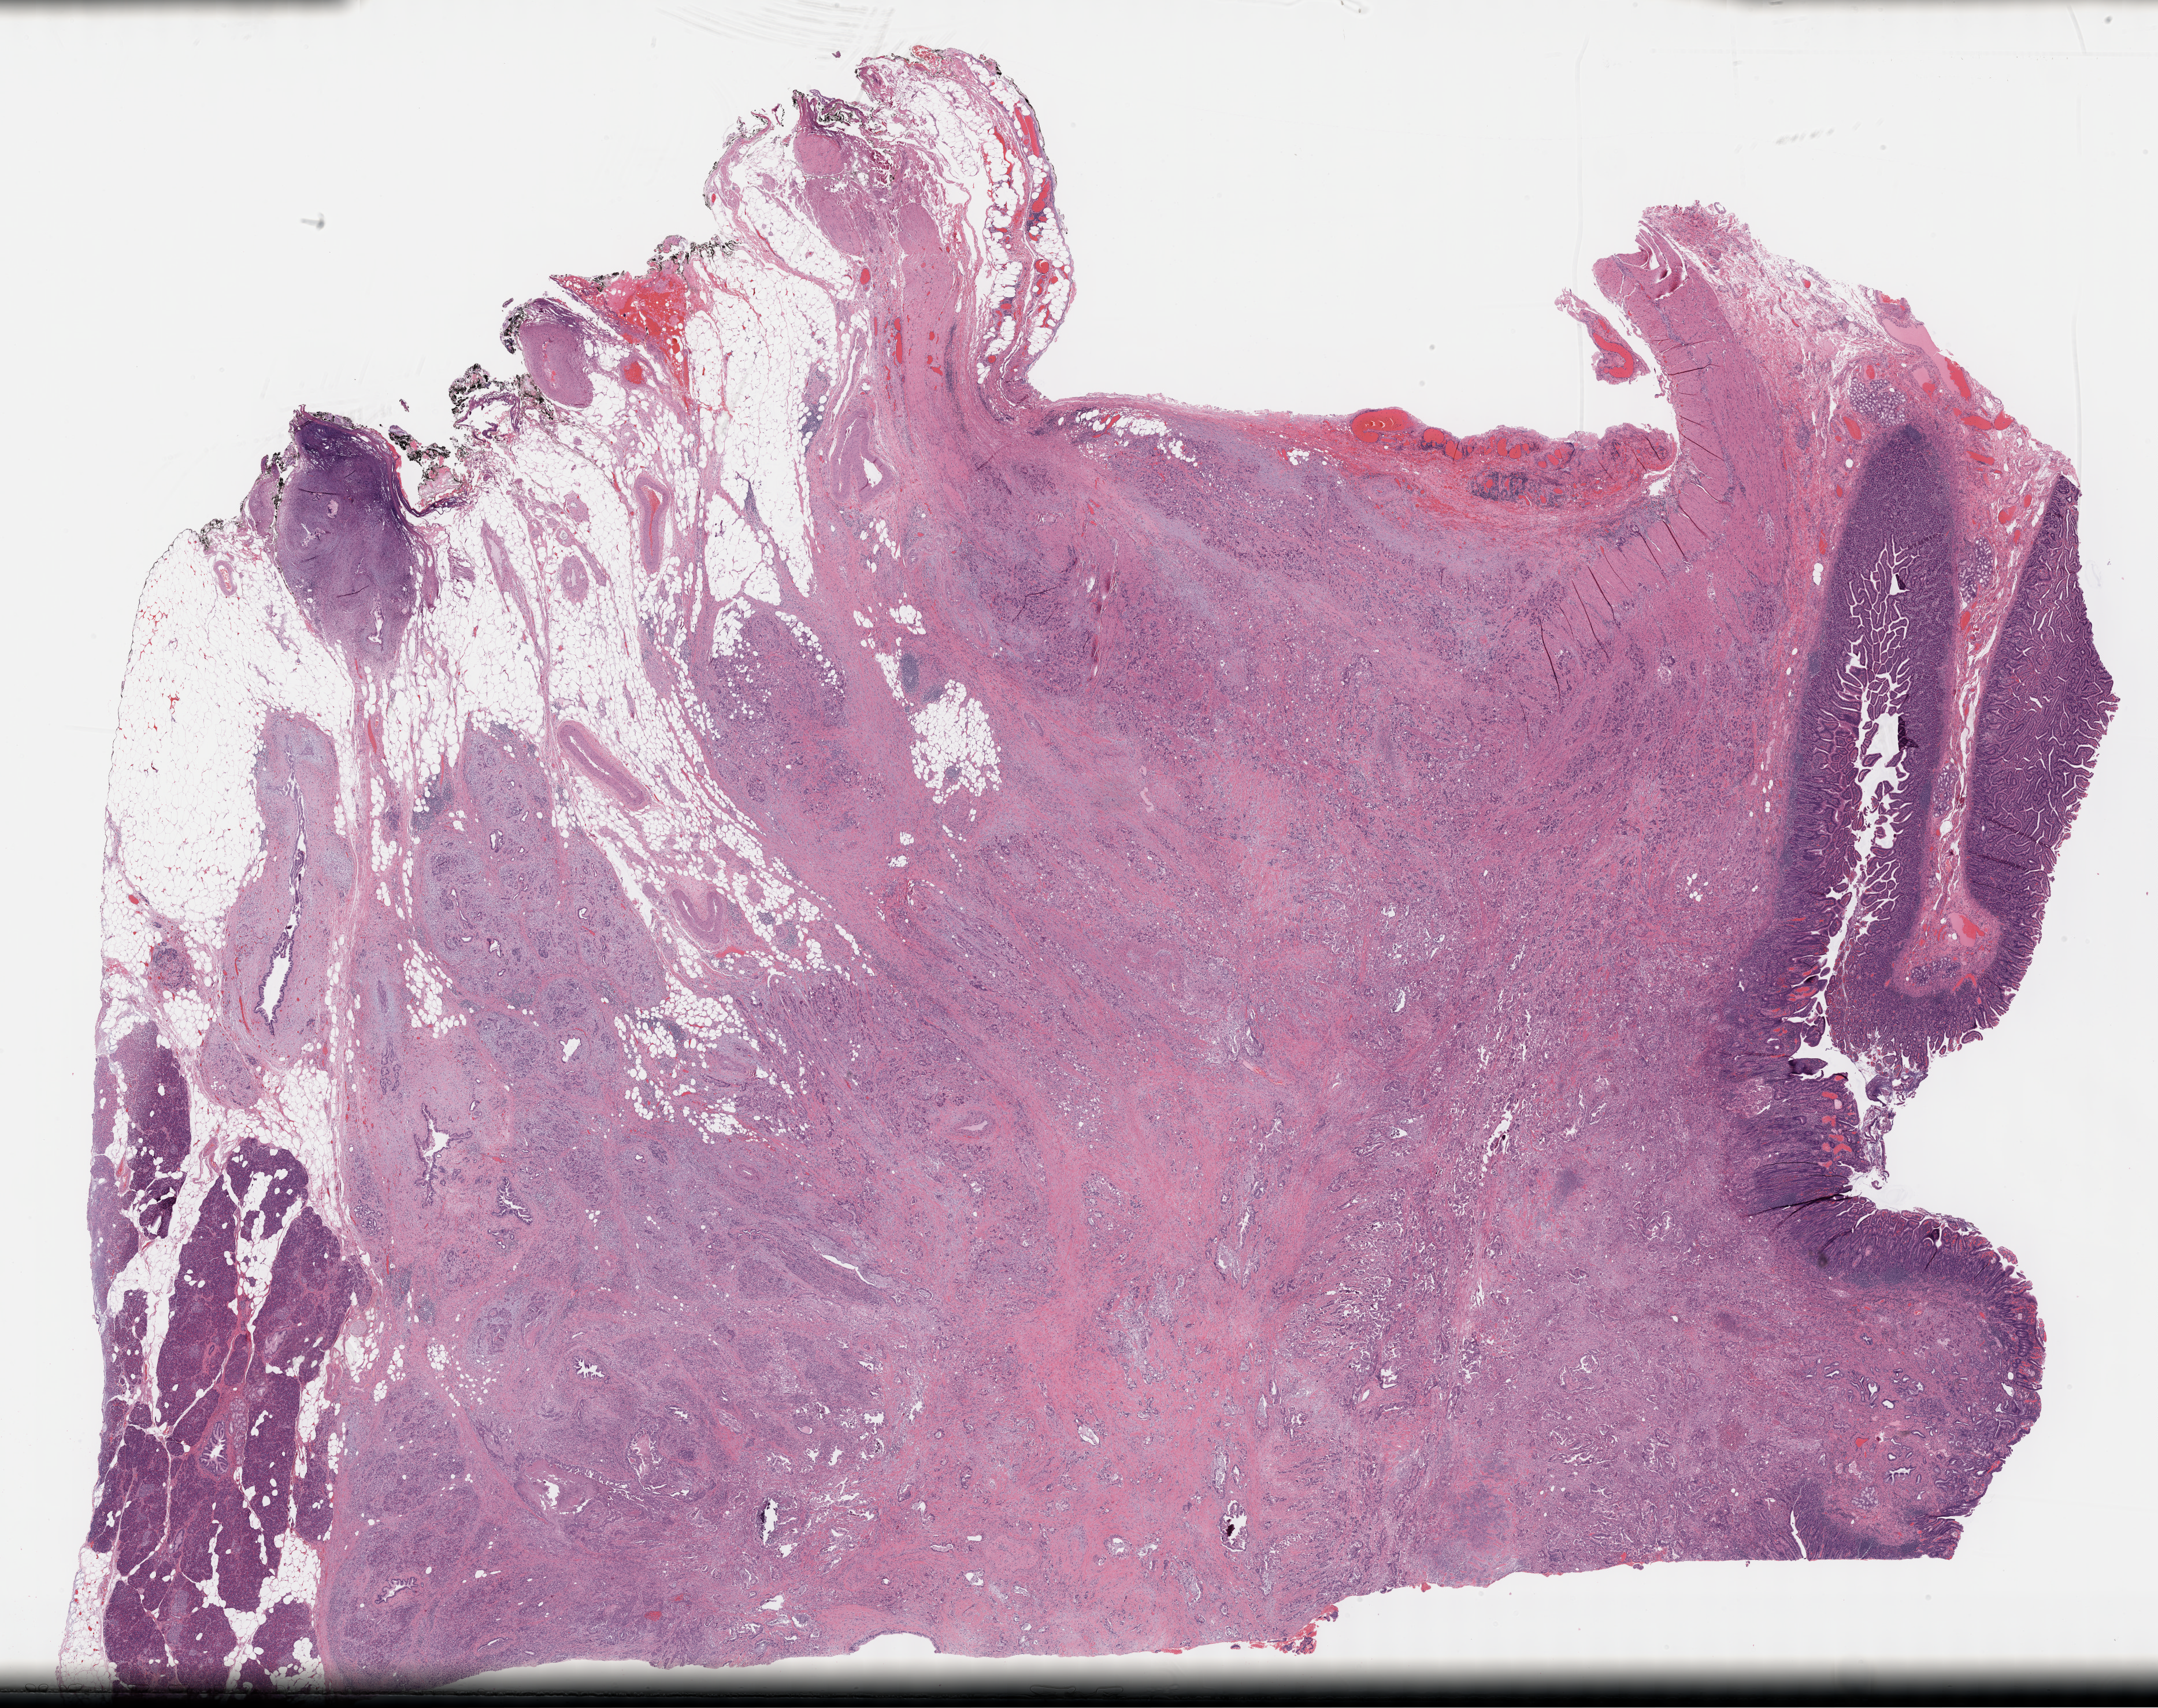
Digitized Hematoxylin and eosin (H&E) stained tissue section (whole slide) — shown as a low-resolution overview of the whole scanned area (about 30.2 x 23.9 mm). Formalin-fixed paraffin-embedded (FFPE) diagnostic section. Sample: primary tumour, pancreas. Patient: female, age at initial diagnosis 64 years. Histologic grade: G3 (poorly differentiated).
Histologic diagnosis: Infiltrating duct carcinoma, NOS (head of pancreas). AJCC pathologic stage: IIB.